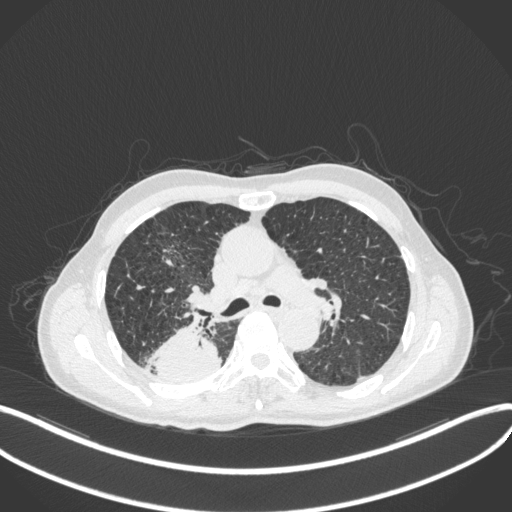
Chest CT, one axial slice; slice 291 of 423 in the series (ordered by position); reconstruction kernel B31f; 120 kVp; lung window (W 1500 / L -600 HU); 512 × 512 image matrix, field of view 400 × 400 mm. Male patient, age 79 years. From the clinical record (not read from this slice): clinical TNM (as recorded): T3 N0 M0.
Structures marked on this image (bounding box drawn by a radiologist):
- lung tumour (recorded histology: adenocarcinoma): bounding box <145,316,223,386> (left, top, right, bottom; pixels)